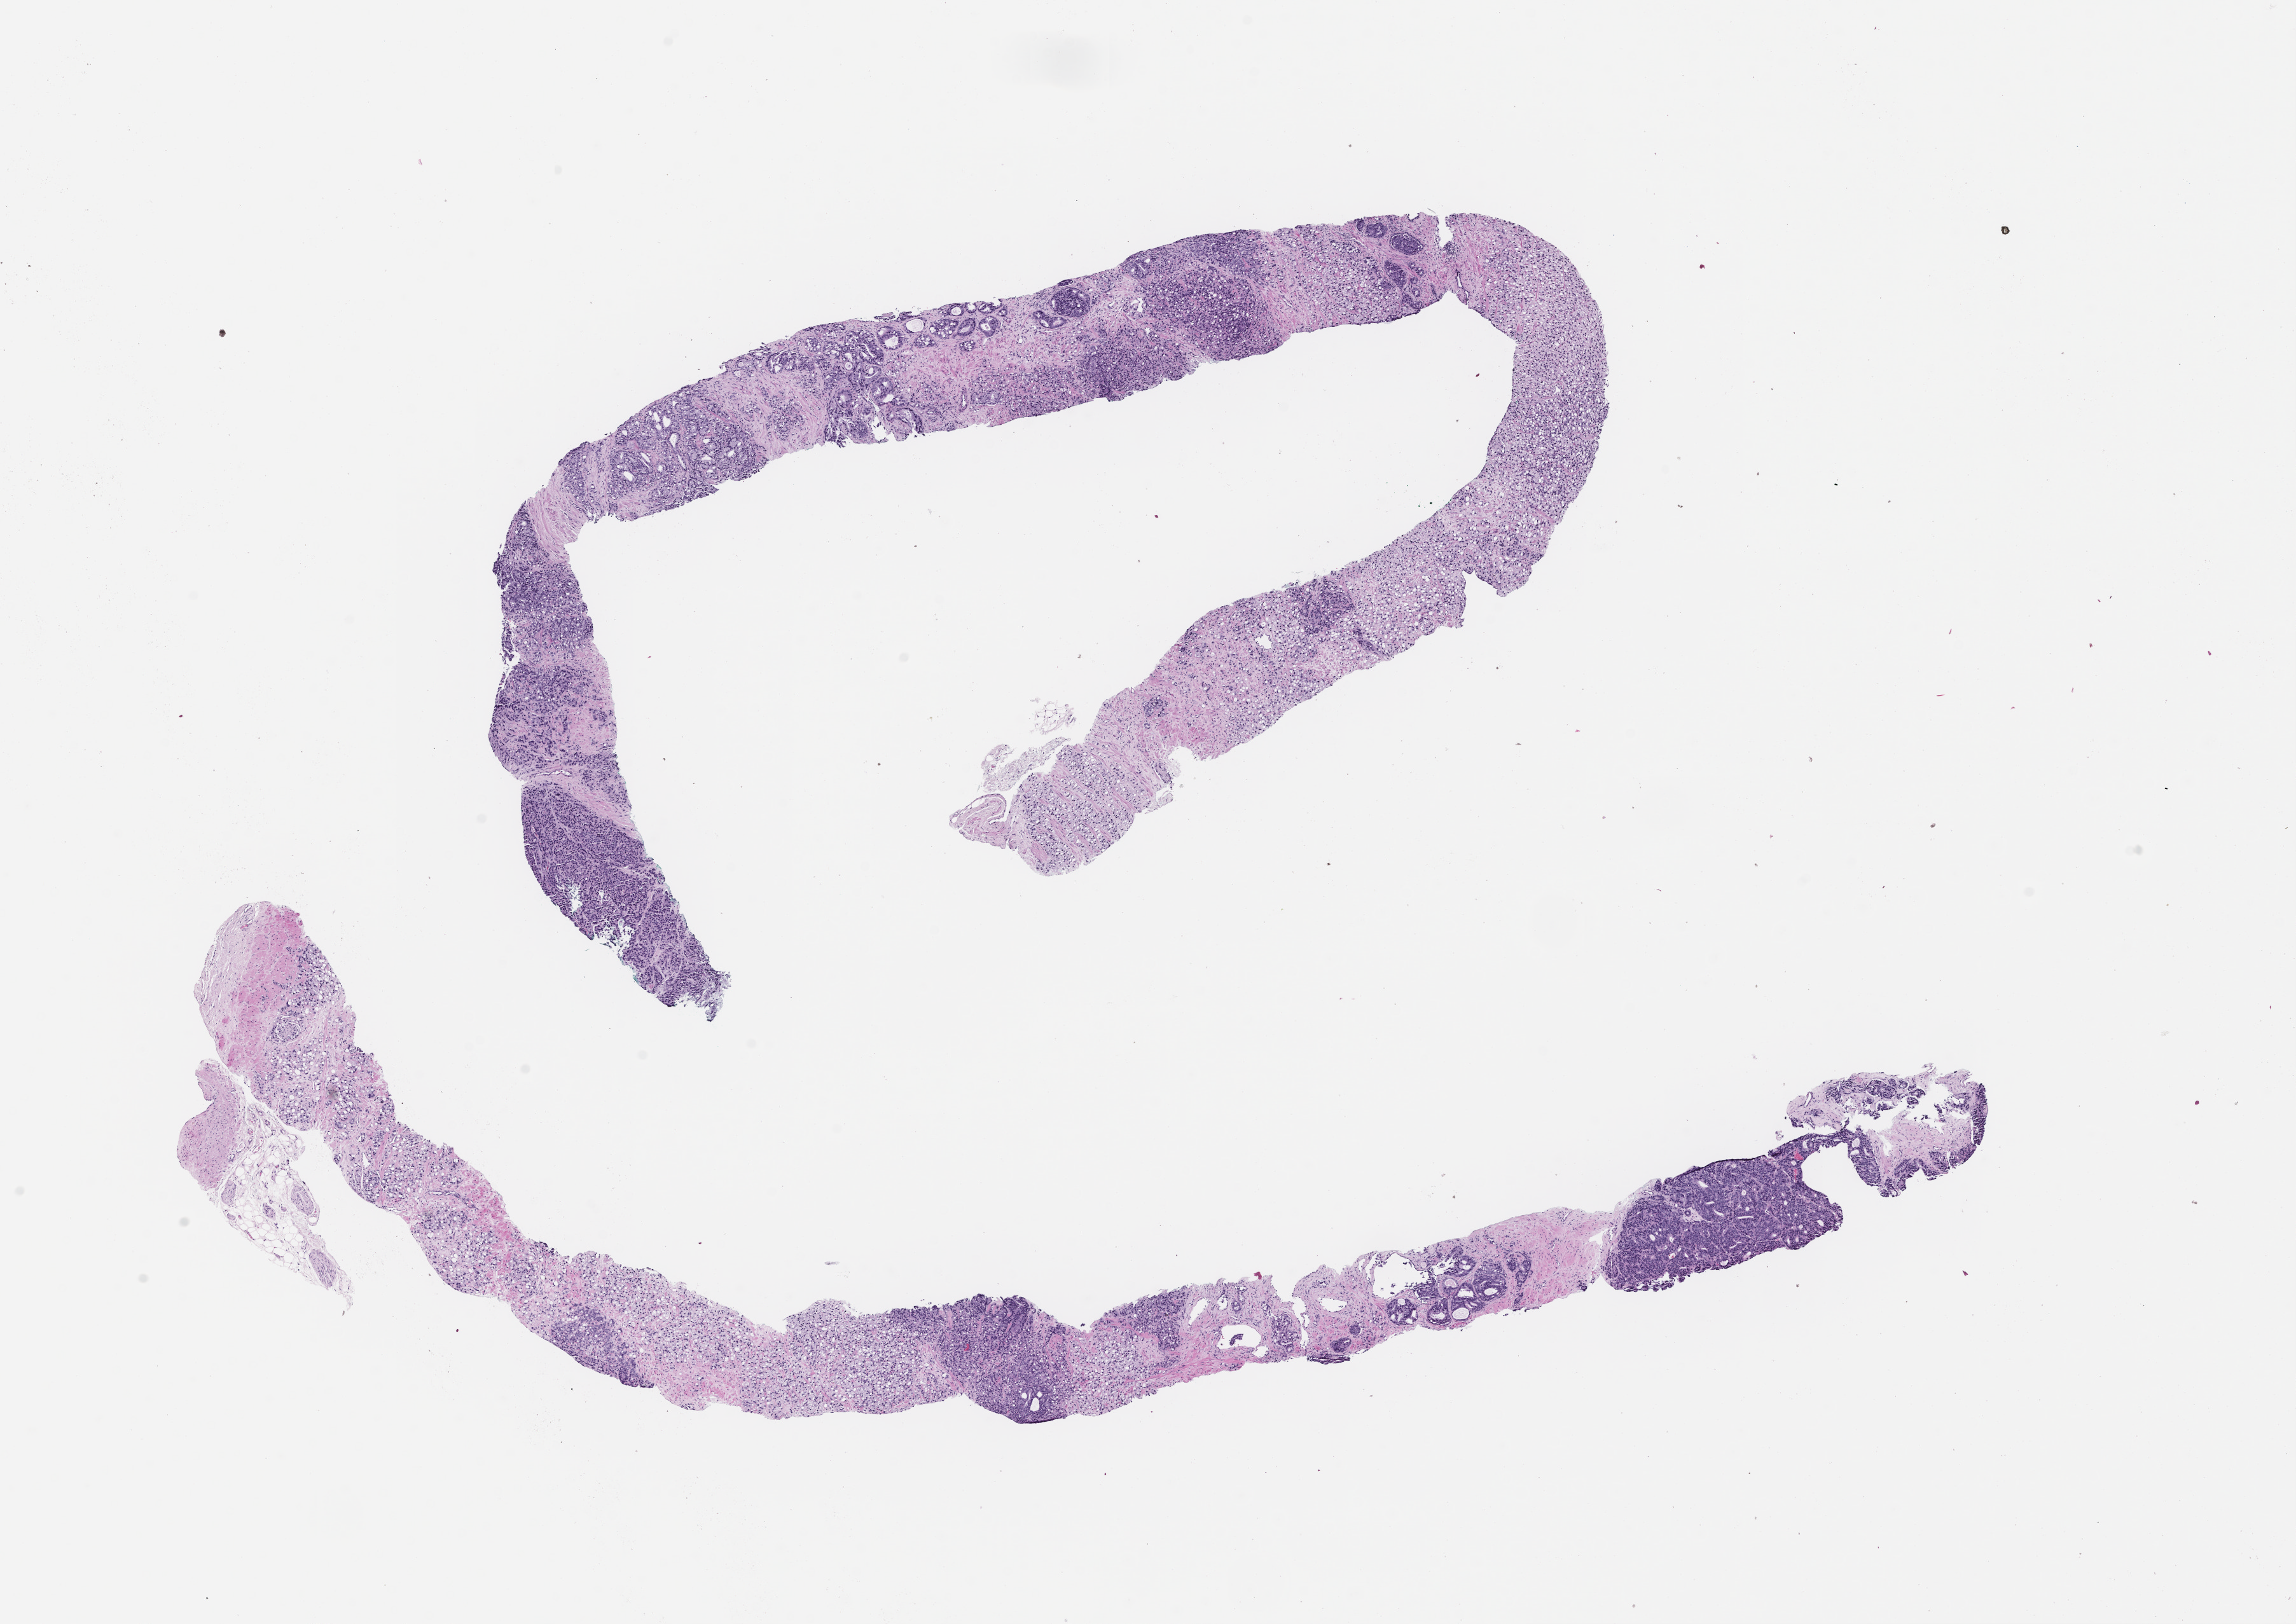
Whole-slide image, haematoxylin and eosin stain — low-resolution overview of the scanned area, about 14.6 x 10.3 mm, FFPE section, specimen time point: archival tissue. Male patient.
This section: metastatic tumor tissue. Primary diagnosis of the patient: Prostate Carcinoma.